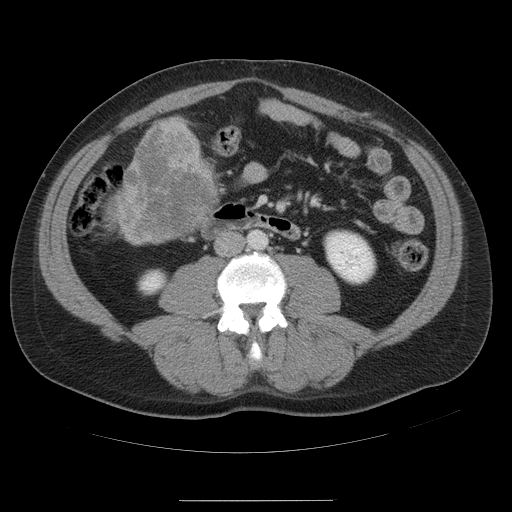
Contrast-enhanced abdominal CT, one axial slice; slice 9 of 54 in the series (ordered by position); intravenous contrast given; soft-tissue window (W 400 / L 40 HU); 5 mm slice thickness; 512 × 512 image matrix. Male patient, age 40 years. From the clinical record (not read from this slice): diagnosis: colorectal cancer liver metastases, imaged before liver resection; multiple liver metastases: no; largest metastasis: 15 cm; disease in both lobes: no.
Annotated regions visible in this slice (manually delineated by an expert):
- liver: bounding box <111,118,219,245> (left, top, right, bottom; pixels)
- liver metastasis: <120,128,216,244>